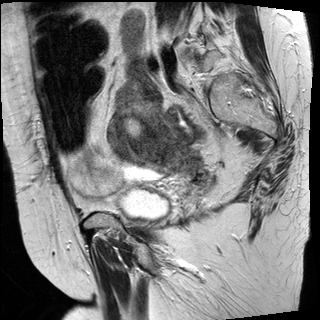
Pelvic MRI for cervical cancer, one sagittal slice; position 21 of 30 along the scan axis; T2-weighted; 1.5 T; TE 89 ms, TR 3810 ms; 4 mm slice thickness; 320 × 320 image matrix. Female patient, age 62 years.
Annotated regions visible in this slice (manually delineated by an expert):
- uterus and cervix: bounding box [x1, y1, x2, y2] px = [106, 103, 205, 174]